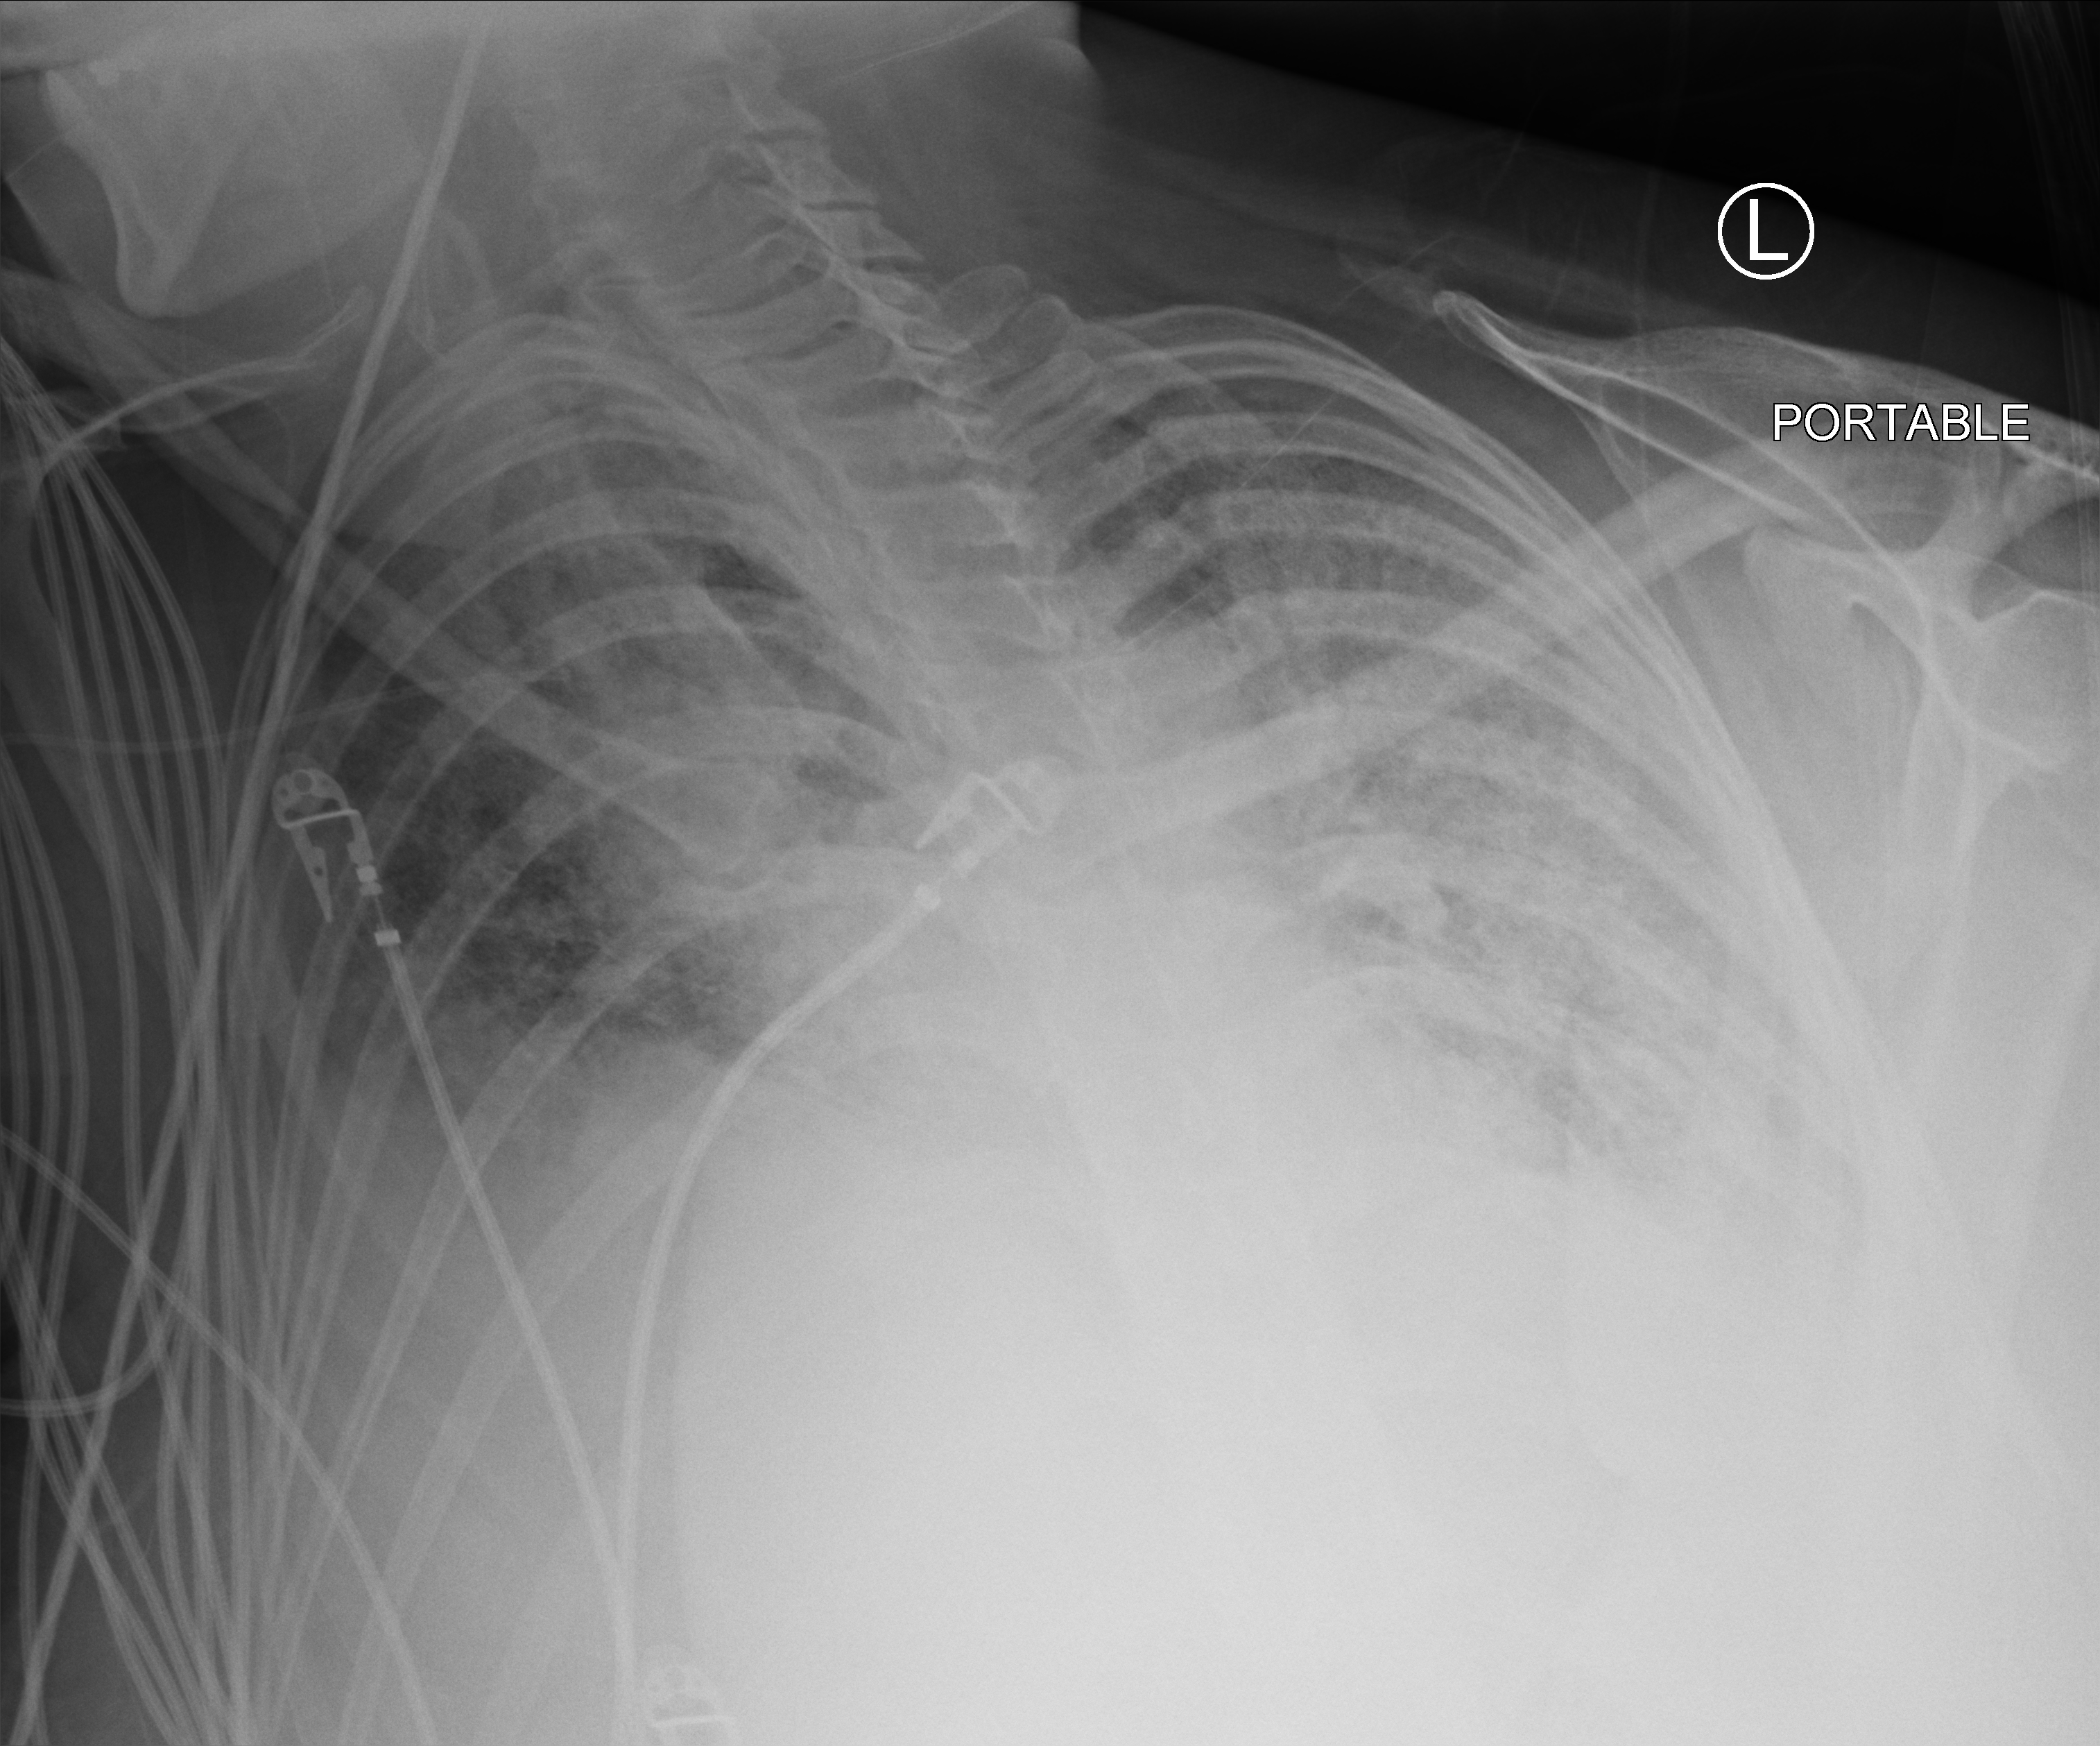
Chest X-ray (portable); anteroposterior (AP) projection. Female patient hospitalised with COVID-19, age 18–59 years.
Hospital-stay facts (about this admission, not read from this image; timing relative to this image not recorded): mechanically ventilated during this hospital stay: yes; hypertension (admission record): no; admitted to intensive care during this hospital stay: yes.